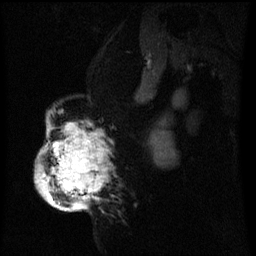
Breast MRI (dynamic contrast-enhanced), one sagittal slice. Position 39 of 60 along the scan axis. Dynamic contrast-enhanced series, image 2 of 3 at this slice position (ordered by acquisition). 1.5 T. TE 4.2 ms, TR 8 ms. 2.2 mm slice thickness. 256 × 256 image matrix. Patient: female, 50 years.
Annotated regions visible in this slice (semi-automatic segmentation, software-assisted and operator-edited):
- analysis volume of interest (the breast-tissue region the enhancement analysis was run in; not a lesion): bounding box (x1, y1, x2, y2) in pixels: (36, 118, 105, 211)
- tumour enhancement mask (voxels above the 70 % enhancement threshold inside the analysis volume of interest): (36, 126, 105, 211)